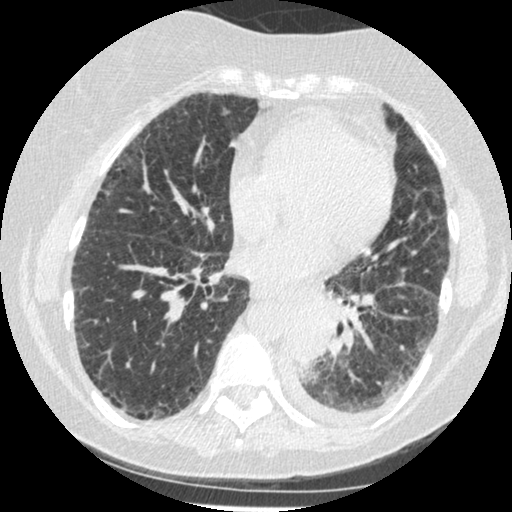
Low-dose screening chest CT, one axial slice. Slice 92 of 341 in the series (ordered by position). Reconstruction kernel STANDARD. 120 kVp. Lung window (W 1500 / L -600 HU). 512 × 512 image matrix, field of view 310 × 310 mm.
Annotated regions visible in this slice (expert manual segmentation):
- lesion 1 (tumor, lower lobe of left lung): box from (x=289, y=312) to (x=330, y=368) px